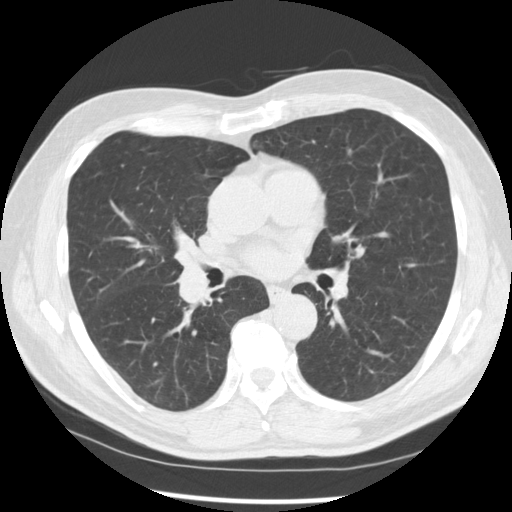
Low-dose screening chest CT, axial slice. First (baseline) screen. Lung window (W 1500 / L -600 HU). 2.5 mm slice thickness. Male participant, aged 67 years at enrolment. Current smoker at enrolment.
Expert reader's lesion annotation, bounding box [x1, y1, x2, y2] px = [159, 247, 228, 312]. The exam's reader record, not a measurement of the box and not confirmed to be the same lesion: non-calcified nodule or mass ≥4 mm, left lower lobe, 15 × 15 mm, spiculated (stellate) margins, soft tissue attenuation. Note: the box lies in the patient's right hemithorax on this image, whereas the reader's record names the left lung; they may be different findings. Official screen result: positive, change unspecified: nodule(s) >= 4 mm or enlarging nodule(s), mass(es), or other non-specific abnormalities suspicious for lung cancer. Participant outcome: lung cancer diagnosed 49 days after this screen — squamous cell carcinoma, NOS, right middle lobe, poorly differentiated (G3), stage IIB (AJCC 6th edition), 35 mm at pathology.